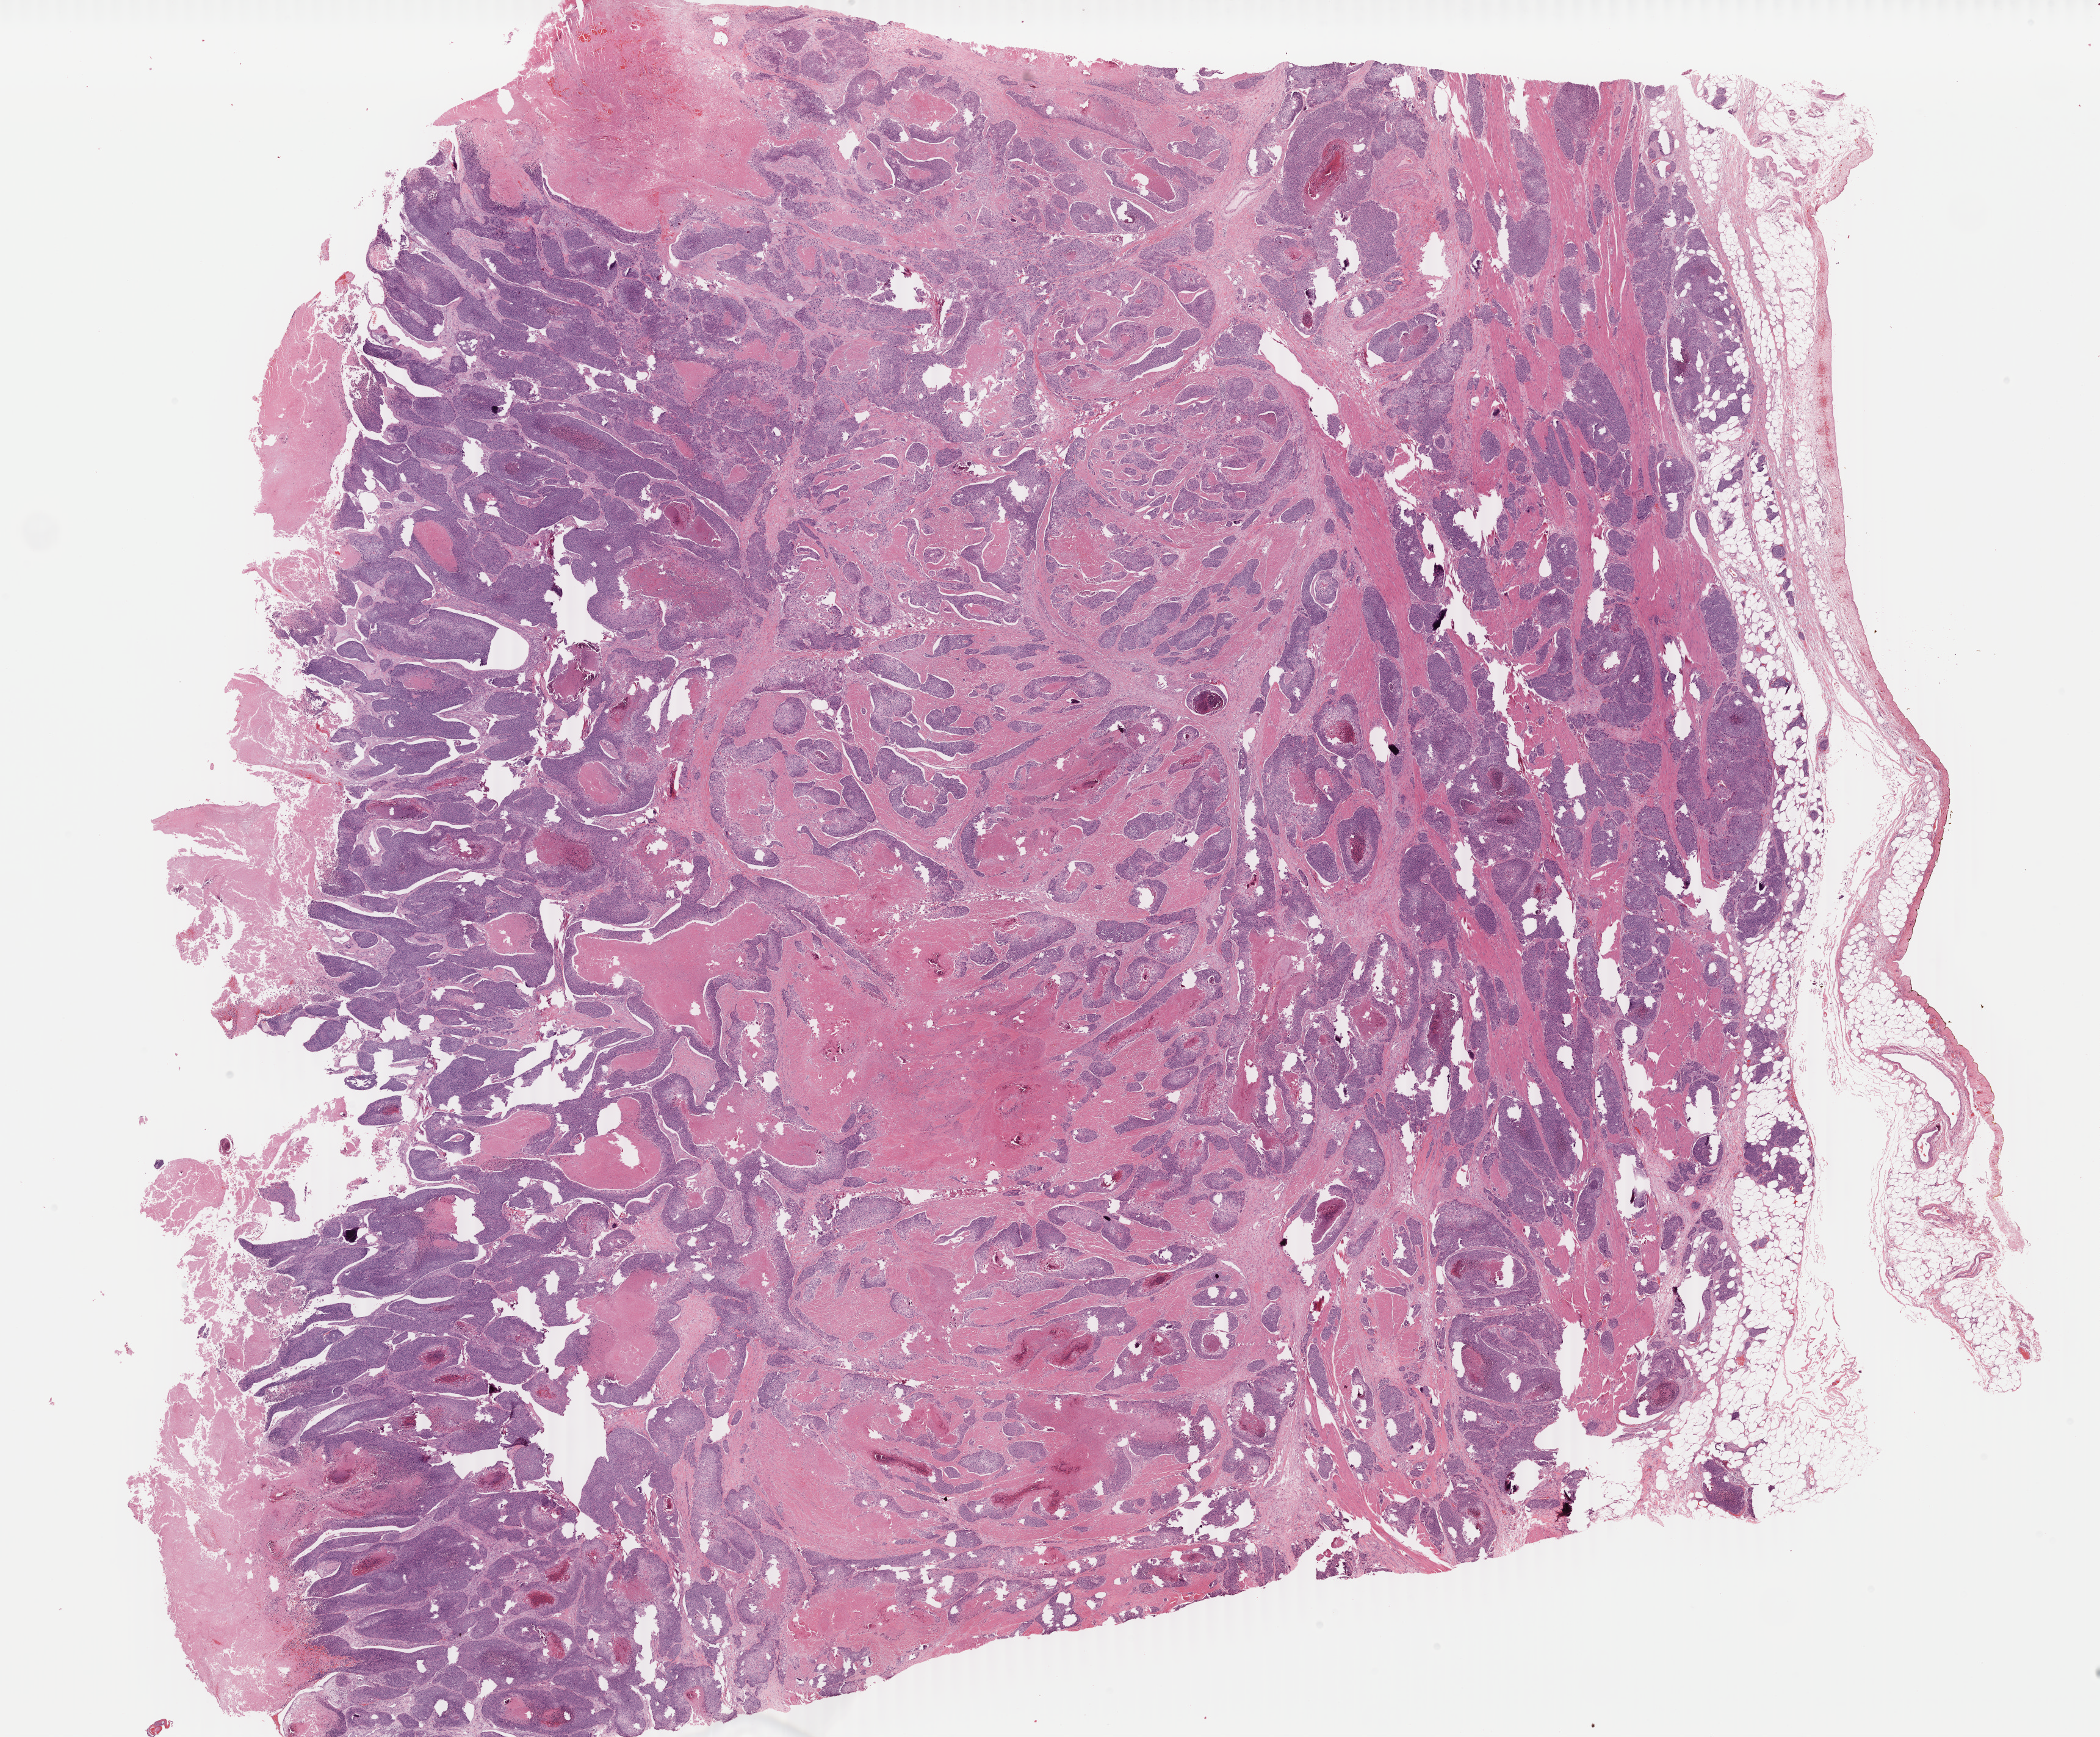
Whole-slide histology image, H&E — a low-resolution overview of the entire scanned area, about 27.4 x 22.6 mm; formalin-fixed paraffin-embedded (FFPE) diagnostic section; primary tumour sample from the bladder. Male patient; age at initial diagnosis 75 years. Histologic grade: high grade.
AJCC pathologic stage: III (6th edition). Pathologic diagnosis: Transitional cell carcinoma.